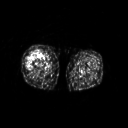
FDG PET of an extremity soft-tissue mass (from a PET/CT study), one axial slice; slice 221 of 311 in the series (ordered by position); 3.27 mm slice thickness; 128 × 128 image matrix, field of view 500 × 500 mm. Patient: female, 57 years. Case-level facts recorded for this patient, not image findings: histological type: pleiomorphic undifferentiated sarcoma; grade: high; site of the primary tumour: right quadricep.
Annotated regions visible in this slice (expert contour drawn on MRI and transferred to this co-registered scan by the dataset authors):
- tumour plus oedema (research contour): bounding box [x1, y1, x2, y2] px = [26, 51, 41, 68]